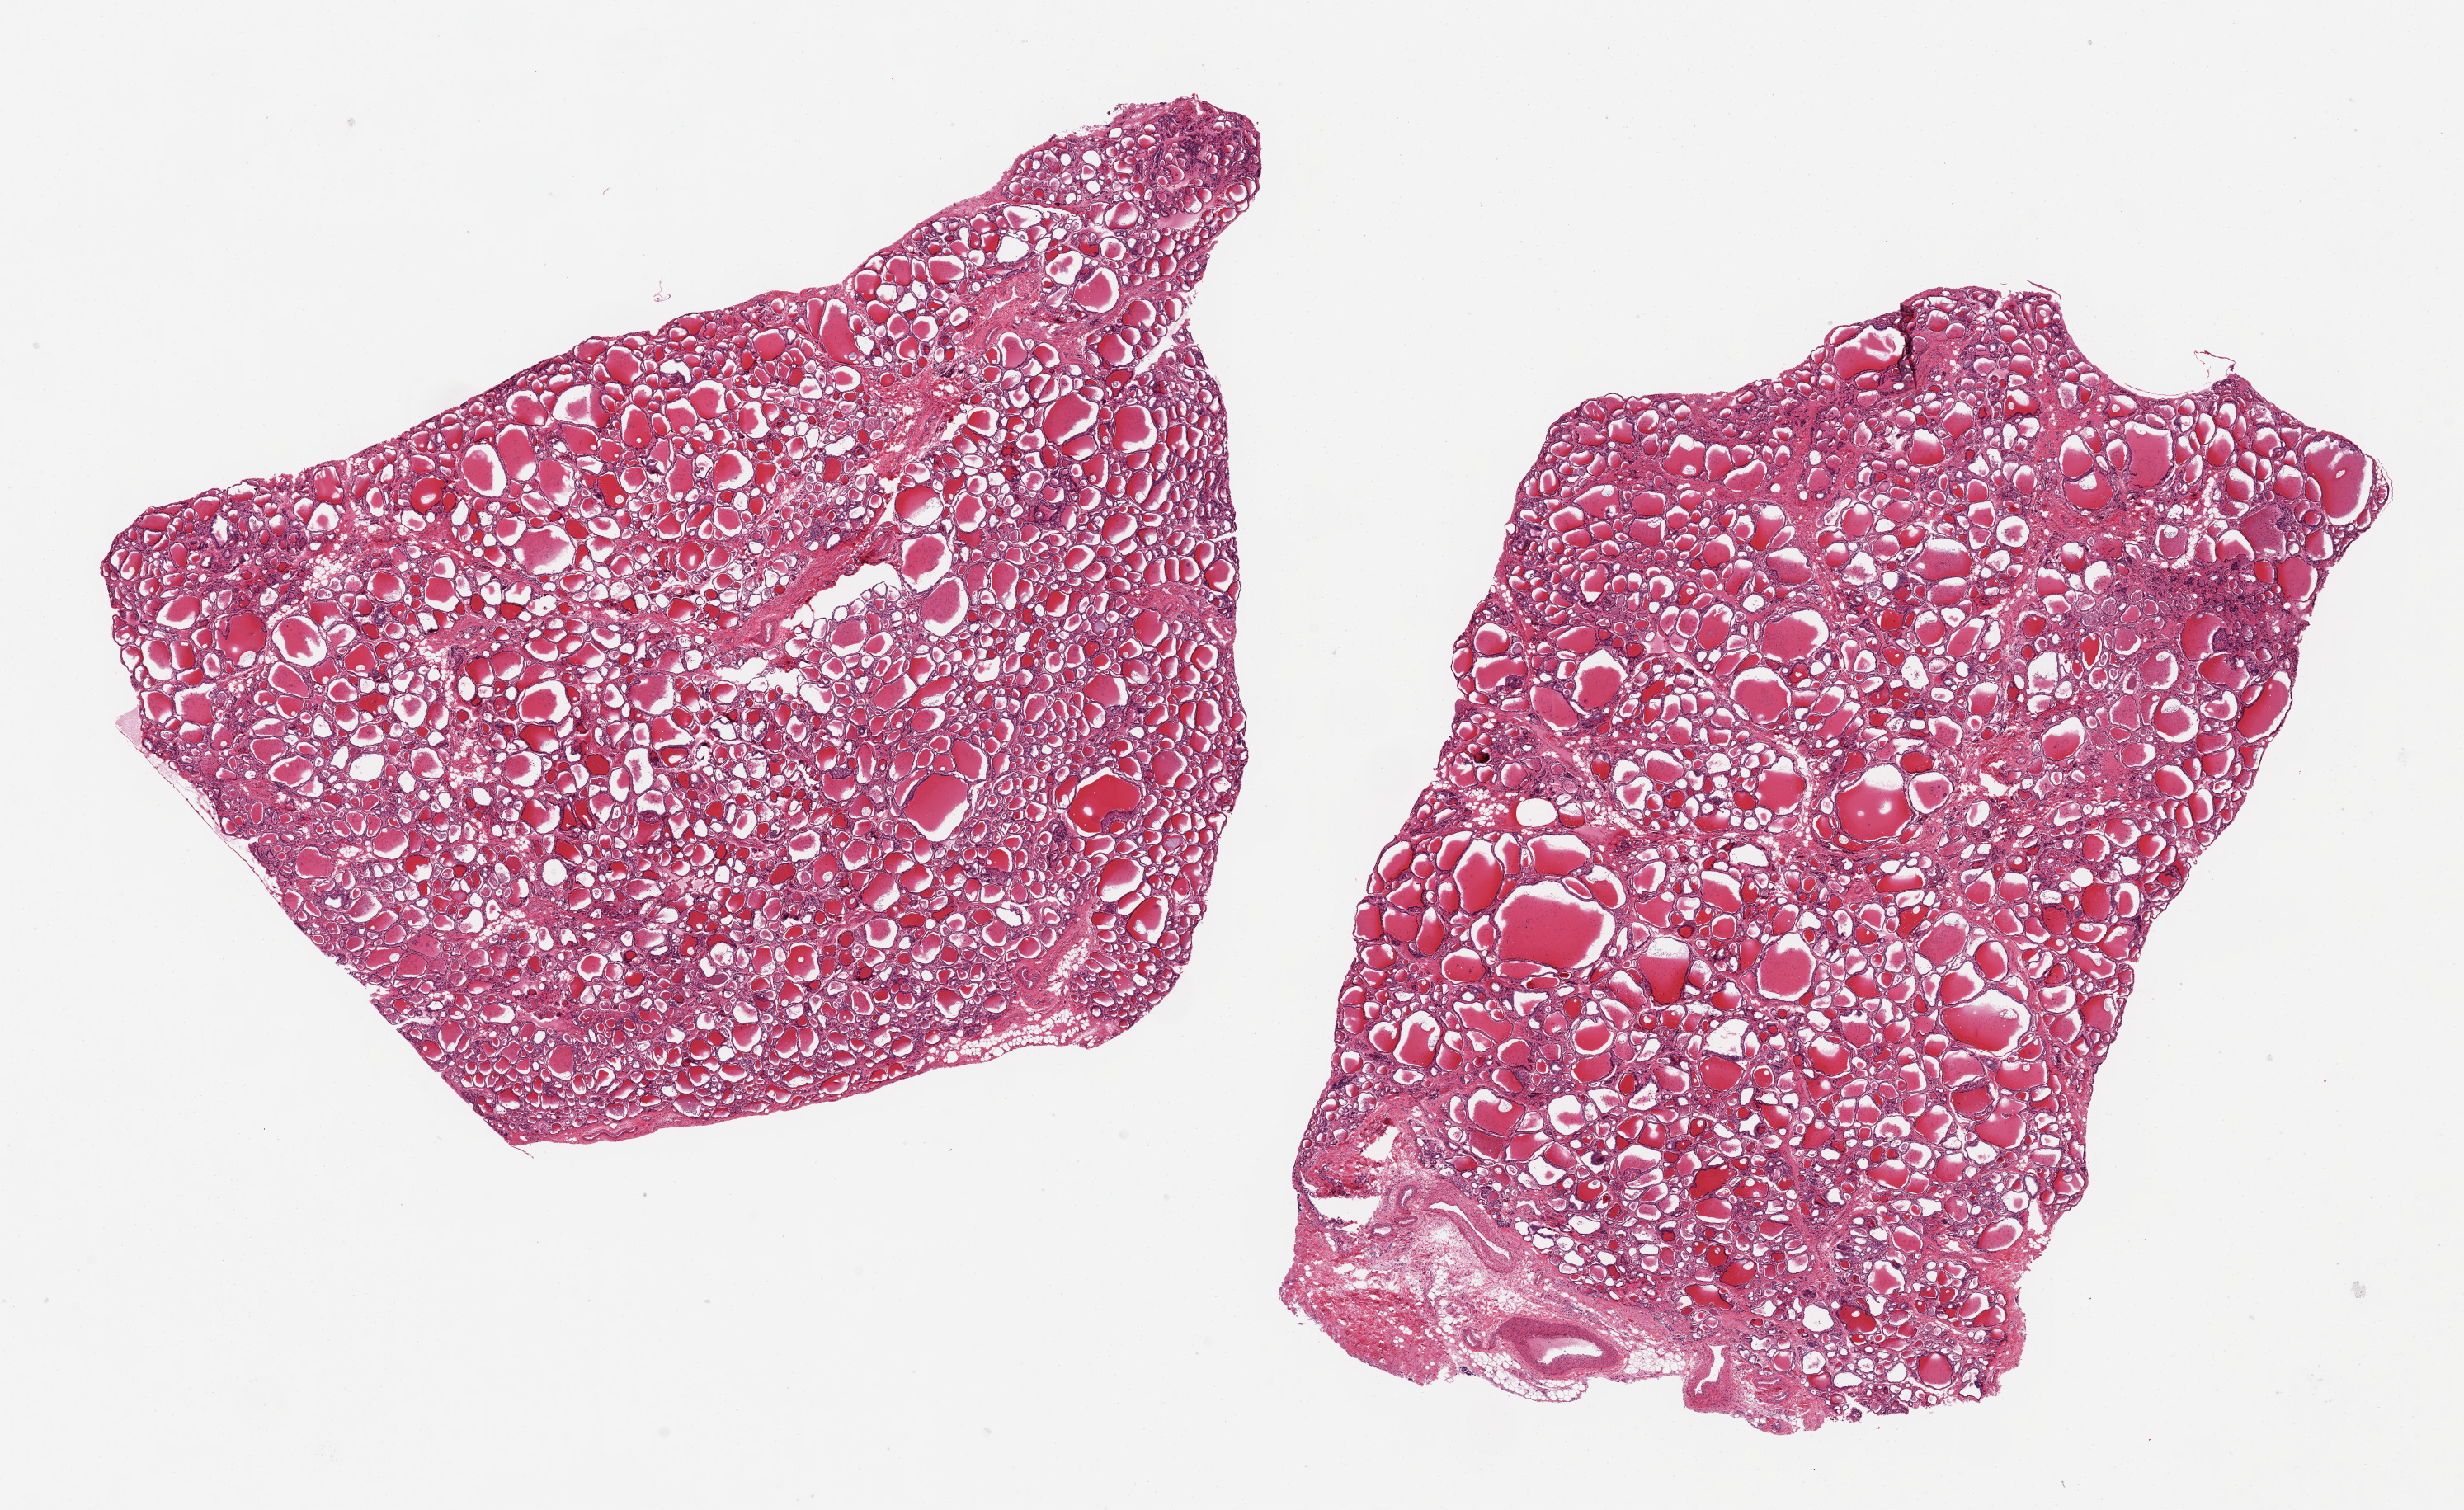
Hematoxylin and eosin (H&E) whole-slide image, whole scanned area (about 23.6 x 14.5 mm) shown as a low-resolution overview. PAXgene-fixed paraffin-embedded (PFPE) section. Section of thyroid (target tissue). Tissue donor sample. Male donor.
Reviewer comment on this tissue sample: 2 aliquots, ~1.5x7.5mm.